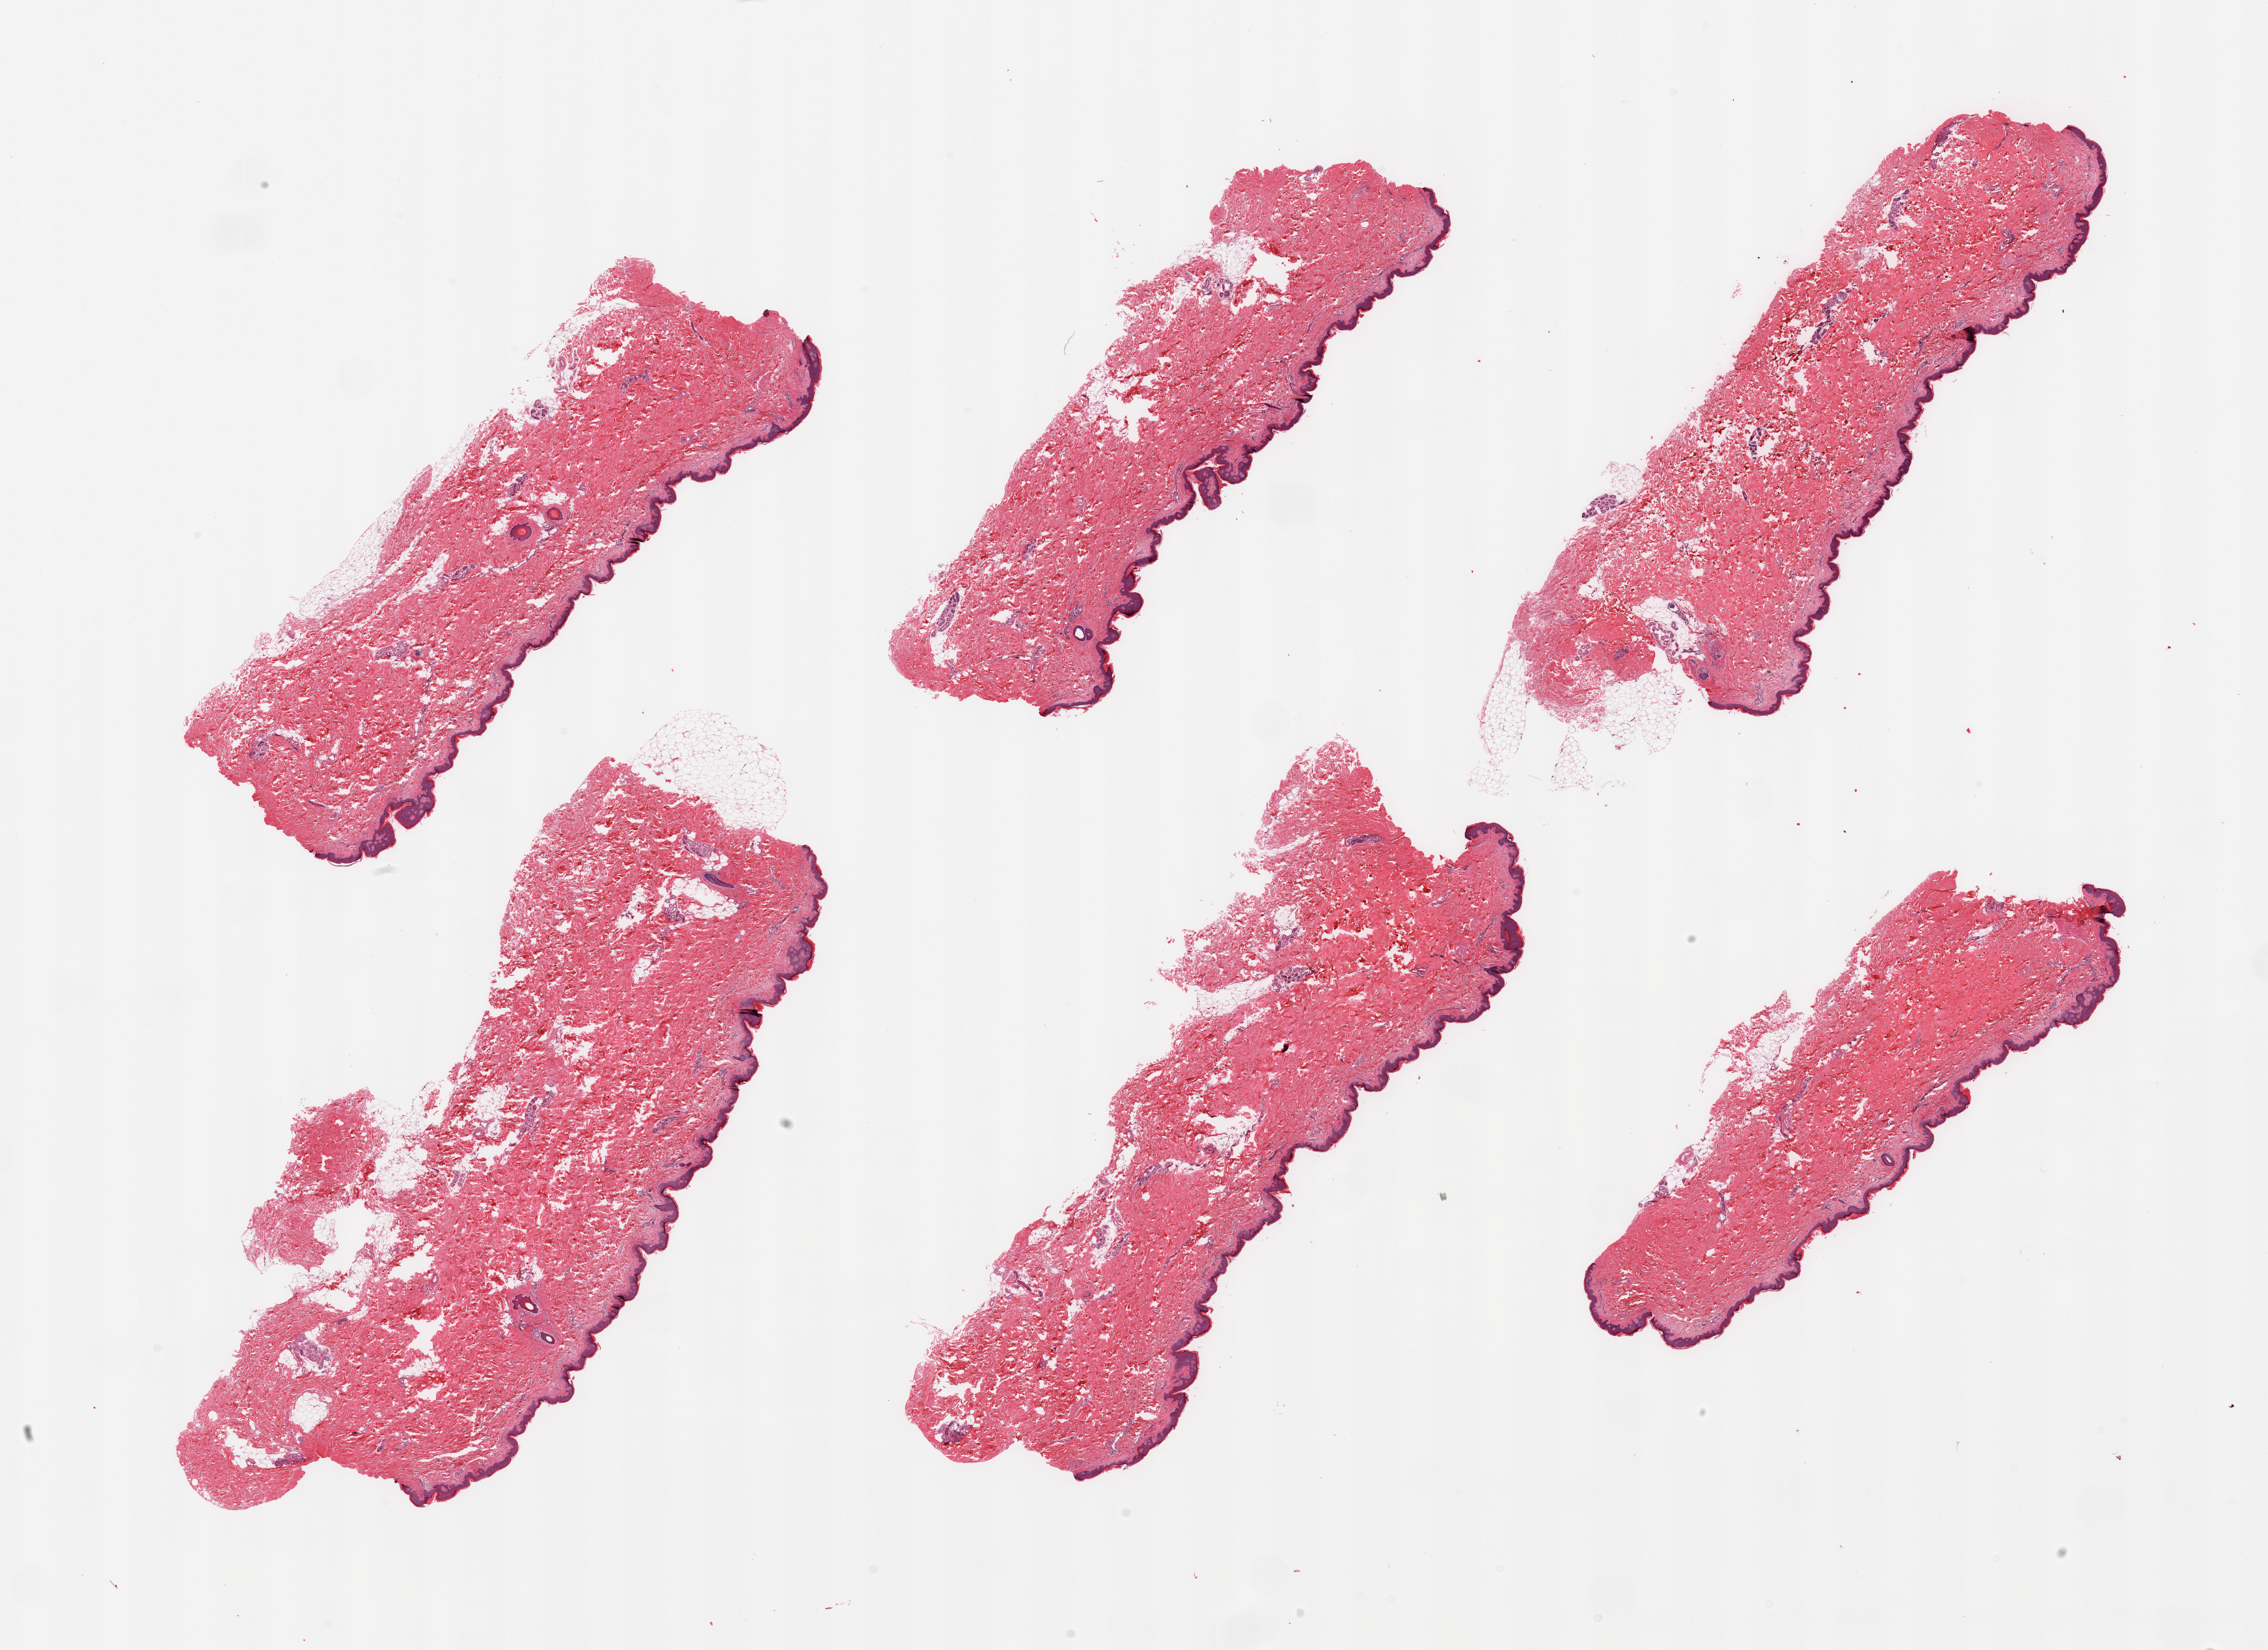
Digitized H&E-stained section, low-resolution overview of the scanned area, about 27.6 x 20.1 mm. PAXgene-fixed, paraffin-embedded tissue. Section of skin of lower leg (target tissue). Donor tissue sample. Donor sex: male.
Reviewer comment on this tissue sample: 6 pieces; relatively well trimmed, includes ~5% internal/external fat, epidermis measures 37 microns.